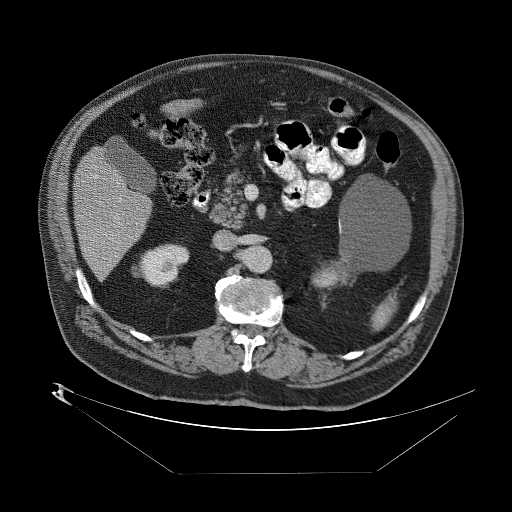
Contrast-enhanced abdominal CT (liver protocol), one axial slice; slice 28 of 89 in the series (ordered by position); reconstruction kernel STANDARD; 140 kVp; one of 2 acquisitions stored at this slice position; soft-tissue window (W 400 / L 40 HU); 2.5 mm slice thickness; 512 × 512 image matrix. Case-level facts recorded for this patient, not image findings: diagnosis: hepatocellular carcinoma (patient treated with transarterial chemoembolisation; whether this scan precedes or follows treatment is not stated here); TNM stage (as recorded): Stage-II; Child-Pugh class: B; tumour nodularity: multinodular.
Outlined on this slice (semi-automatically segmented with operator editing):
- abdominal aorta: bounding box [x1, y1, x2, y2] px = [246, 248, 270, 273]
- liver parenchyma outside the tumour (the mass and vessels are separate outlines, so this box may not span the whole liver): [70, 142, 150, 280]
- liver vessels: [84, 213, 129, 255]